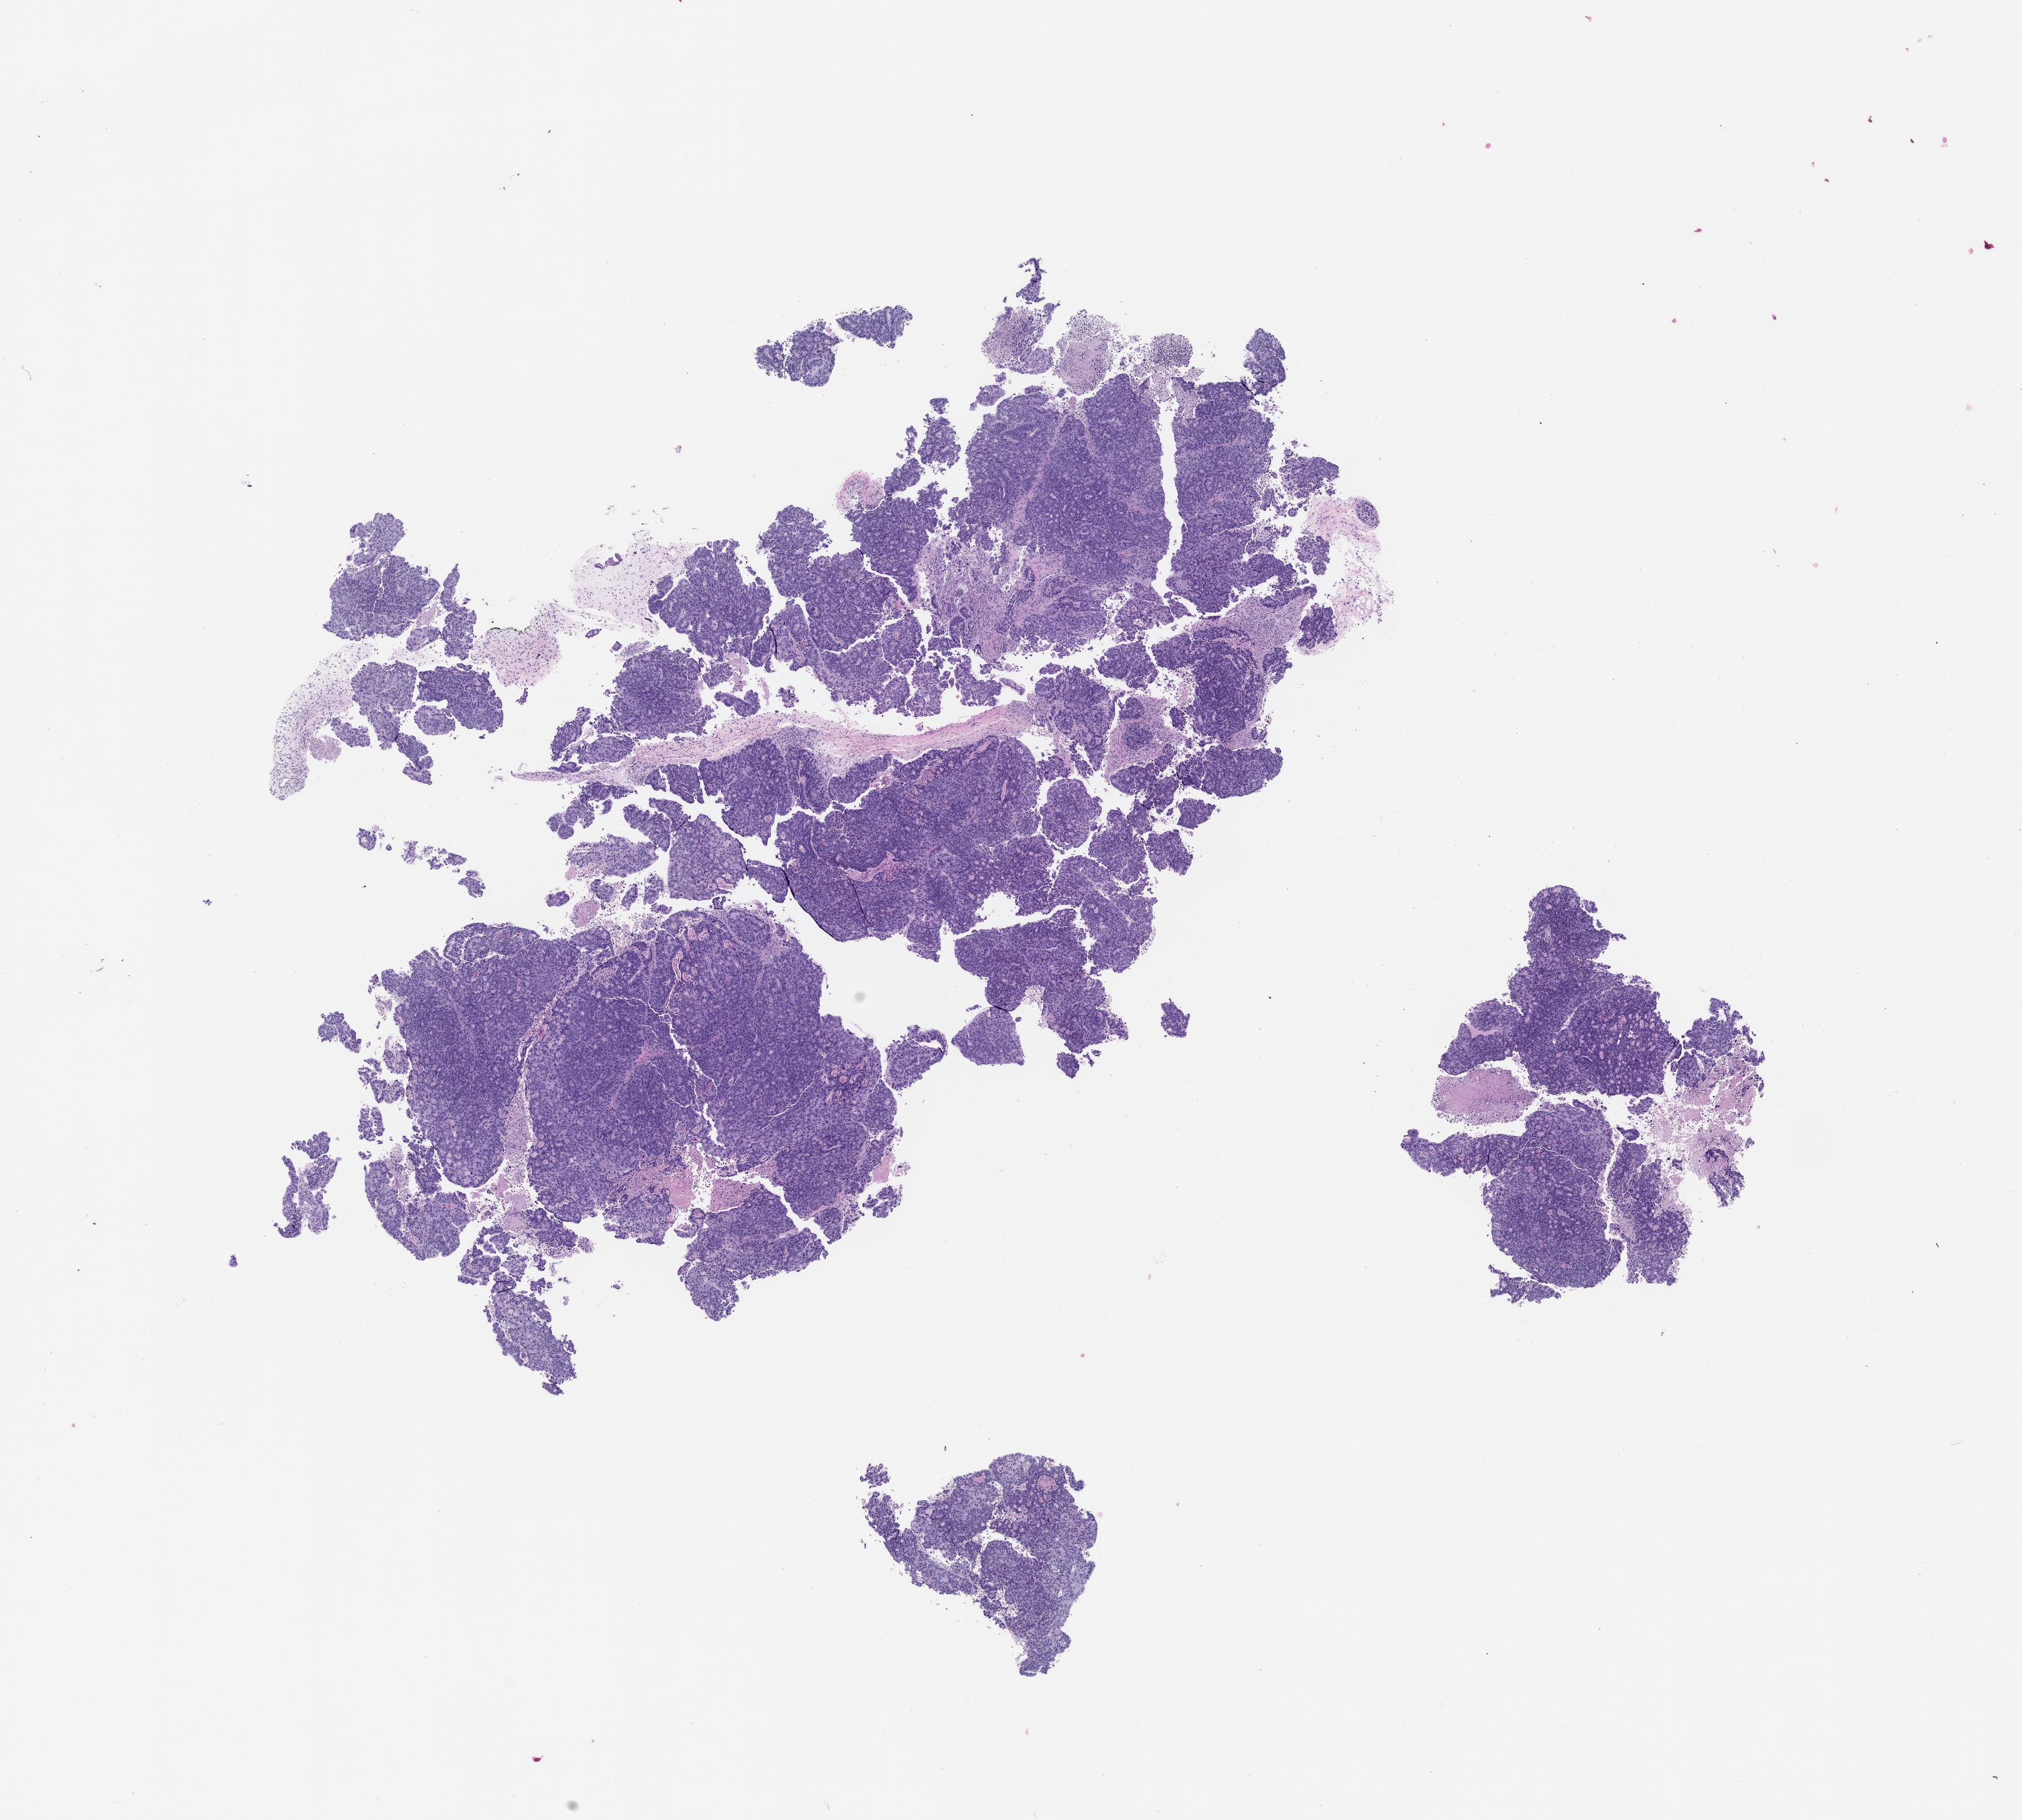
Haematoxylin and eosin whole-slide image of a patient-derived xenograft (PDX) tumor grown in a mouse, passage 0 — low-resolution overview of the scanned area, about 13.0 x 11.7 mm; formalin-fixed paraffin-embedded section; tumor site category: colon.
Originating patient diagnosis: Colon Adenocarcinoma.